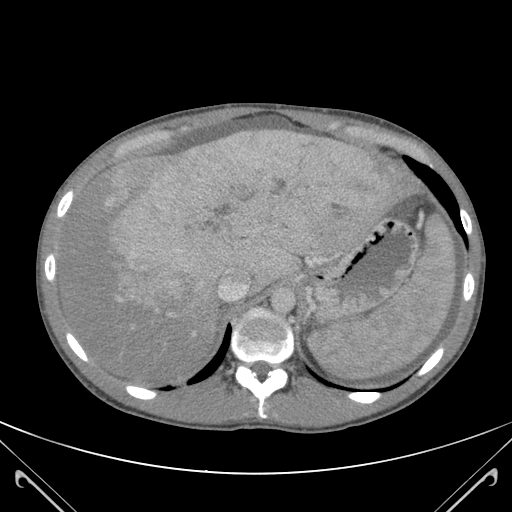
Contrast-enhanced abdominal CT (liver protocol), one axial slice. Position 91 of 118 along the scan axis. 120 kVp. Soft-tissue window (W 400 / L 40 HU). 512 × 512 image matrix, field of view 380 × 380 mm. Case-level facts recorded for this patient, not image findings: diagnosis: hepatocellular carcinoma (patient treated with transarterial chemoembolisation; whether this scan precedes or follows treatment is not stated here); TNM stage (as recorded): Stage-IIIB; Child-Pugh class: A; tumour nodularity: uninodular.
Structures marked on this image (semi-automatic segmentation, software-assisted and operator-edited):
- abdominal aorta: bounding box [x1, y1, x2, y2] px = [274, 288, 297, 311]
- liver parenchyma outside the tumour (the mass and vessels are separate outlines, so this box may not span the whole liver): [62, 128, 423, 378]
- mass: [98, 129, 407, 318]
- liver vessels: [119, 270, 249, 301]